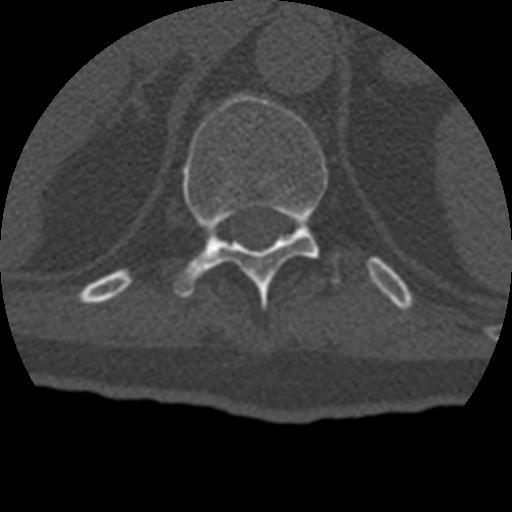
CT including the spine, one axial slice. Slice 195 of 399 in the series (ordered by position). Reconstruction kernel STANDARD. 120 kVp. Bone window (W 1800 / L 400 HU). 1.25 mm slice thickness. 512 × 512 image matrix. Patient age 69 years. From the clinical record (not read from this slice): primary cancer: prostate.
Annotated regions visible in this slice (semi-automatic segmentation, software-assisted and operator-edited):
- T11 vertebra: bounding box (x1, y1, x2, y2) in pixels: (175, 94, 329, 297)